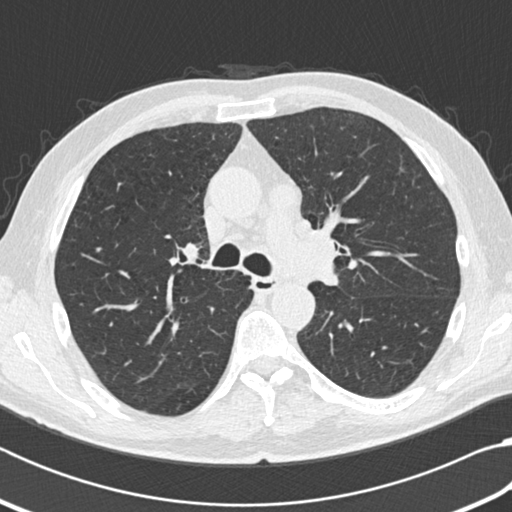
Low-dose screening chest CT, axial slice. Third annual screen. Lung window (W 1500 / L -600 HU). Standard (soft-tissue) reconstruction kernel (B30f). 512 × 512 image matrix. Male participant, aged 64 years at enrolment. Current smoker at enrolment.
Expert-annotated lung lesion, bounding box <253,175,303,220> (left, top, right, bottom; pixels). Screening reader's record for this exam: no non-calcified nodule ≥4 mm recorded. Official screen result: negative screen, significant abnormalities not suspicious for lung cancer. Lung cancer was diagnosed 163 days after this screen: small cell carcinoma, NOS, mediastinum, stage IV (AJCC 6th edition).